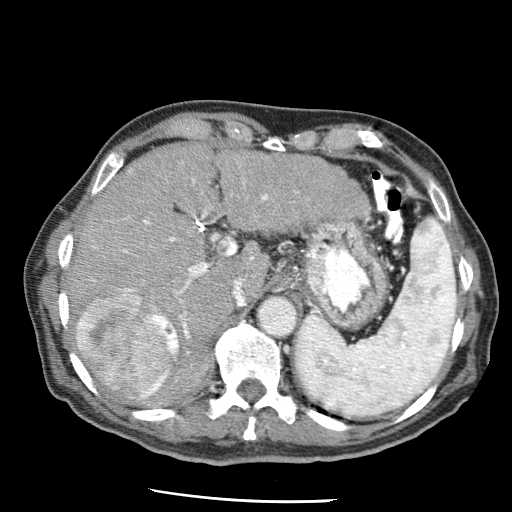
Contrast-enhanced abdominal CT (liver protocol), one axial slice. Slice 42 of 79 in the series (ordered by position). Reconstruction kernel STANDARD. 120 kVp. Soft-tissue window (W 400 / L 40 HU). 512 × 512 image matrix, field of view 320 × 320 mm. From the clinical record (not read from this slice): diagnosis: hepatocellular carcinoma (patient treated with transarterial chemoembolisation; whether this scan precedes or follows treatment is not stated here); TNM stage (as recorded): Stage-IIIA; Child-Pugh class: A.
Outlined on this slice (semi-automatic segmentation, software-assisted and operator-edited):
- liver parenchyma outside the tumour (the mass and vessels are separate outlines, so this box may not span the whole liver): bounding box (x1, y1, x2, y2) in pixels: (66, 144, 370, 404)
- mass: (76, 287, 178, 399)
- liver vessels: (91, 161, 369, 334)